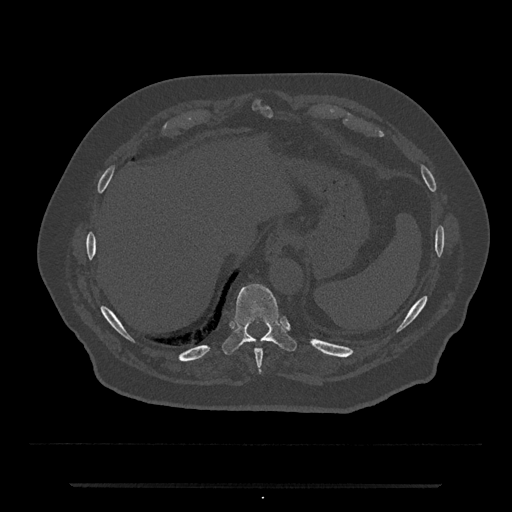
CT including the spine, one axial slice; slice 719 of 797 in the series (ordered by position); reconstruction kernel Br40s/3; 120 kVp; bone window (W 1800 / L 400 HU); 512 × 512 image matrix, field of view 434 × 434 mm. Male patient, age 80 years. Case-level facts recorded for this patient, not image findings: primary cancer: prostate; vertebrae with lytic lesions (as recorded): L1, T11.
Annotated regions visible in this slice (semi-automatically segmented with operator editing):
- T10 vertebra: bounding box [x1, y1, x2, y2] px = [222, 284, 297, 355]
- T9 vertebra: [255, 349, 263, 373]